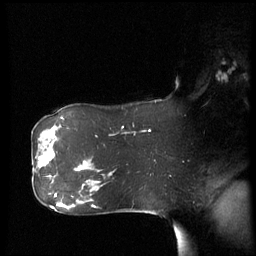
Breast MRI (dynamic contrast-enhanced), one sagittal slice; position 41 of 60 along the scan axis; dynamic contrast-enhanced series, image 2 of 3 at this slice position (ordered by acquisition); 1.5 T; TE 4.2 ms, TR 8.4 ms; 256 × 256 image matrix, field of view 280 × 280 mm. Female patient, age 61 years. From the clinical record (not read from this slice): setting: breast cancer imaged before/during neoadjuvant chemotherapy; receptor status: HR-positive, HER2-negative.
Annotated regions visible in this slice (semi-automatic segmentation, software-assisted and operator-edited):
- analysis volume of interest (the breast-tissue region the enhancement analysis was run in; not a lesion): bounding box <33,142,59,179> (left, top, right, bottom; pixels)
- tumour enhancement mask (voxels above the 70 % enhancement threshold inside the analysis volume of interest): <39,156,50,167>